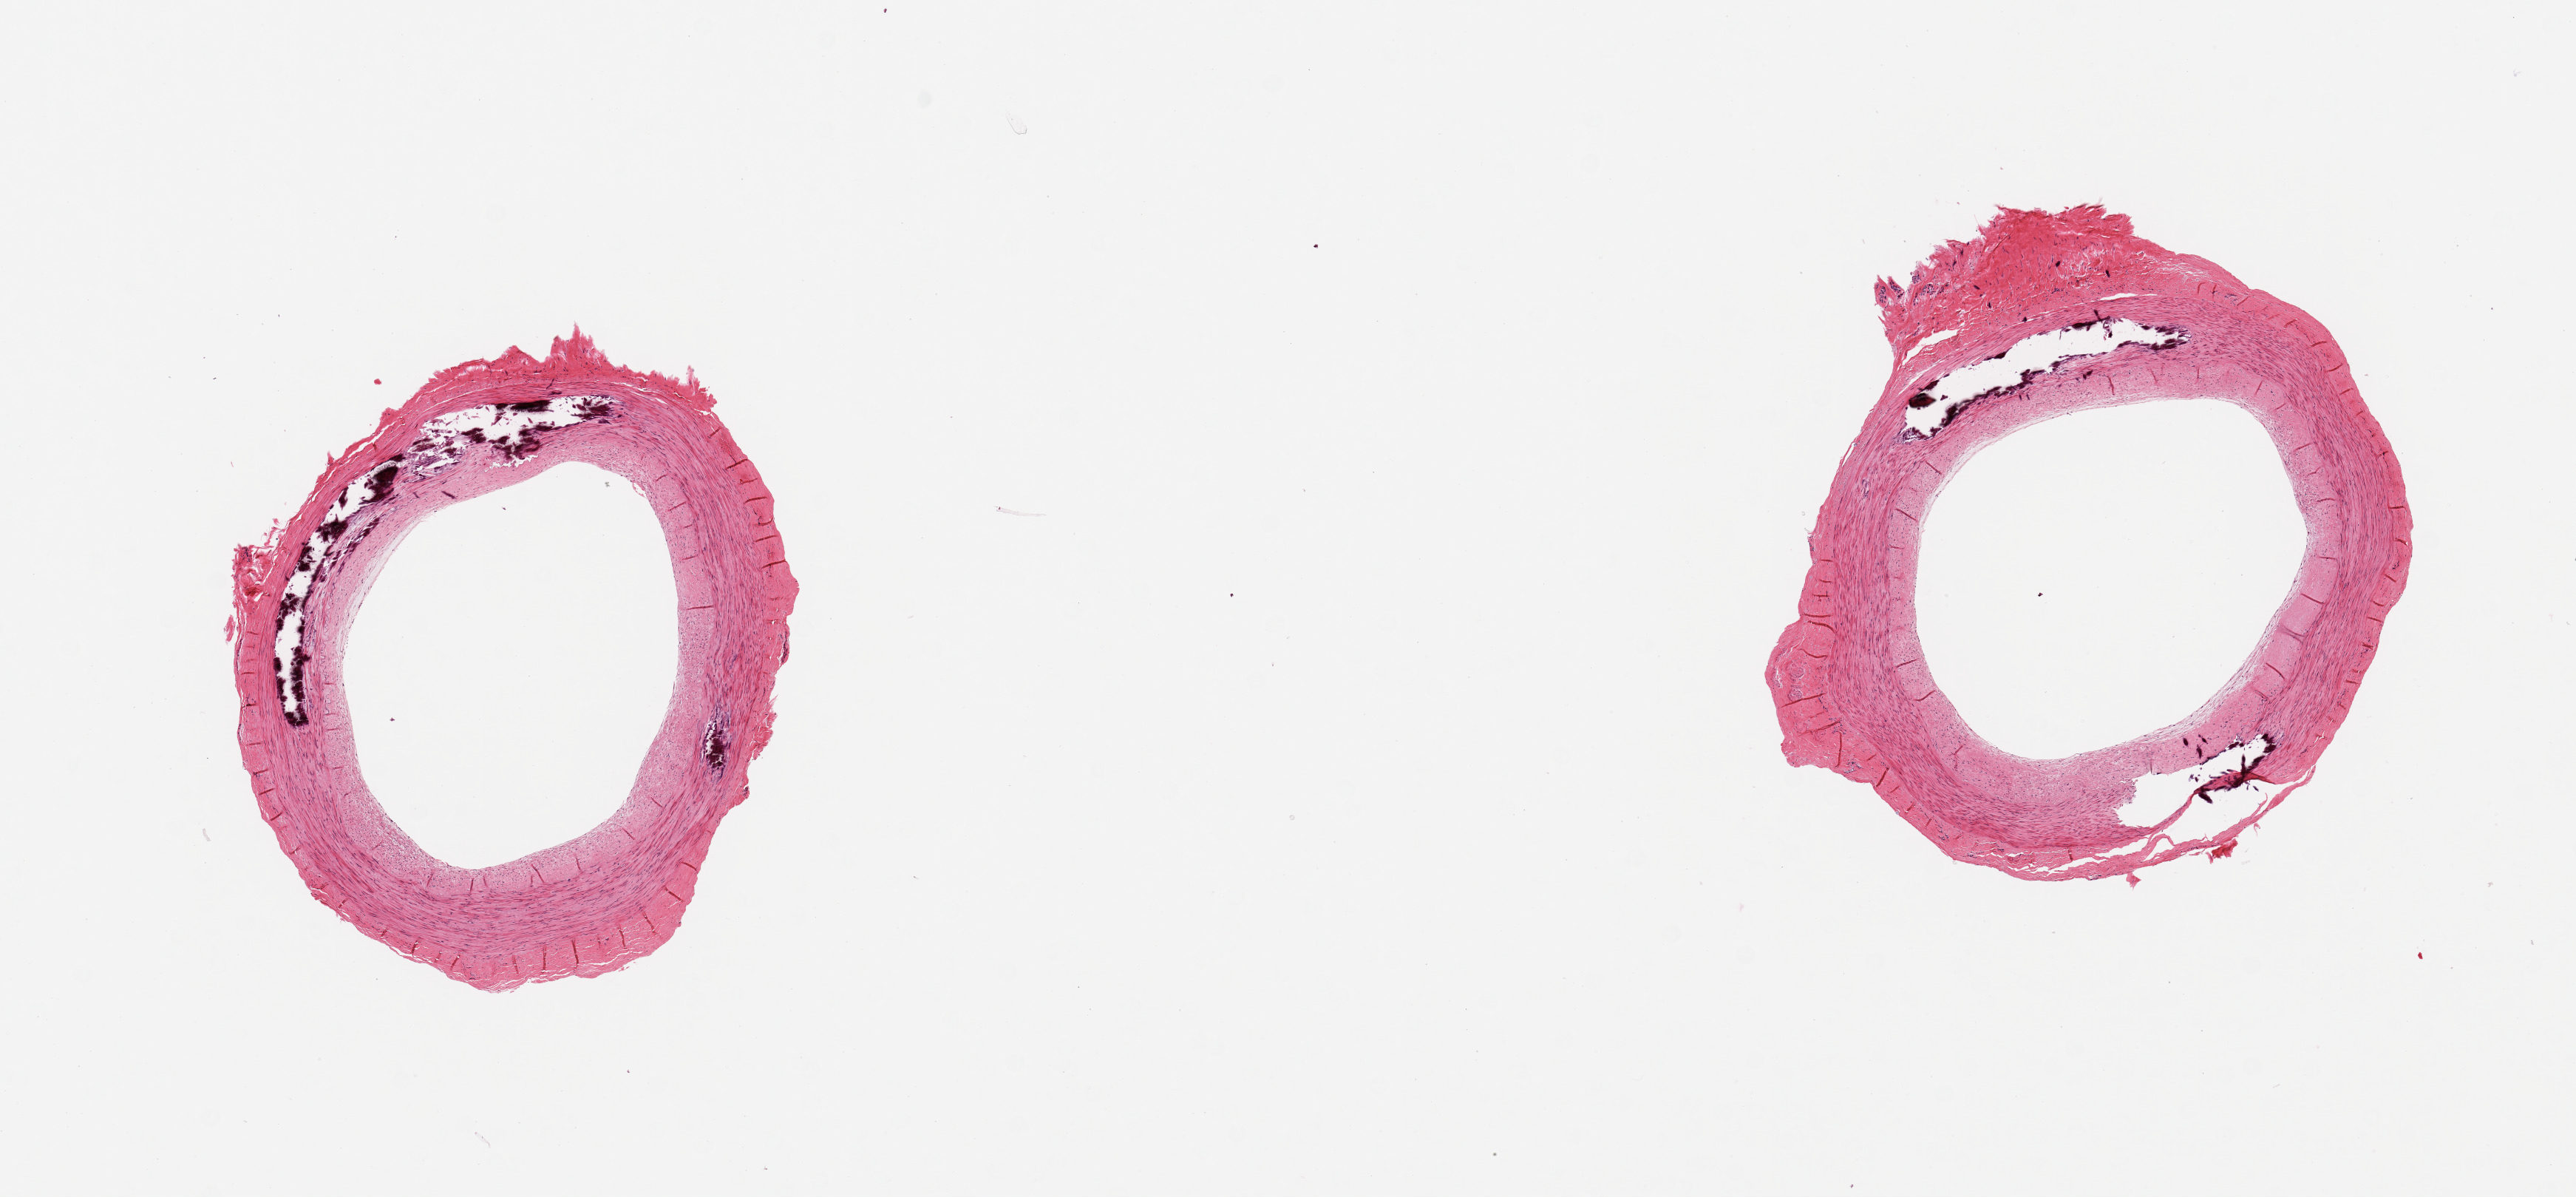
Digitized haematoxylin and eosin-stained section, brightfield — a low-resolution overview of the entire scanned area, about 13.8 x 6.4 mm; PAXgene-fixed, paraffin-embedded tissue; sampled site (target tissue): tibial artery; tissue donor sample. Male donor.
- reviewer comment on this tissue sample: 2 pieces, no significant atherosis or adherent fat; prominent Monckeberg mediial sclerosis